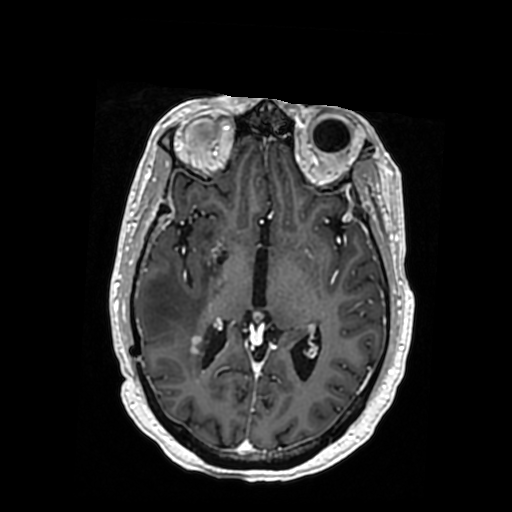
Brain MRI from a brain-tumour surgery series, one axial slice; slice 192 of 364 in the series (ordered by position); T1-weighted post-contrast; 0.5 mm slice thickness; 512 × 512 image matrix, field of view 260 × 260 mm. From the clinical record (not read from this slice): histopathology: Oligodendroglioma; WHO grade: 3; IDH mutation: yes; tumour location: Right Posterior Temporal Inferior Parietal.
Structures marked on this image (expert manual segmentation):
- previous resection cavity: bounding box <216,254,226,266> (left, top, right, bottom; pixels)
- tumour: <155,333,165,350>